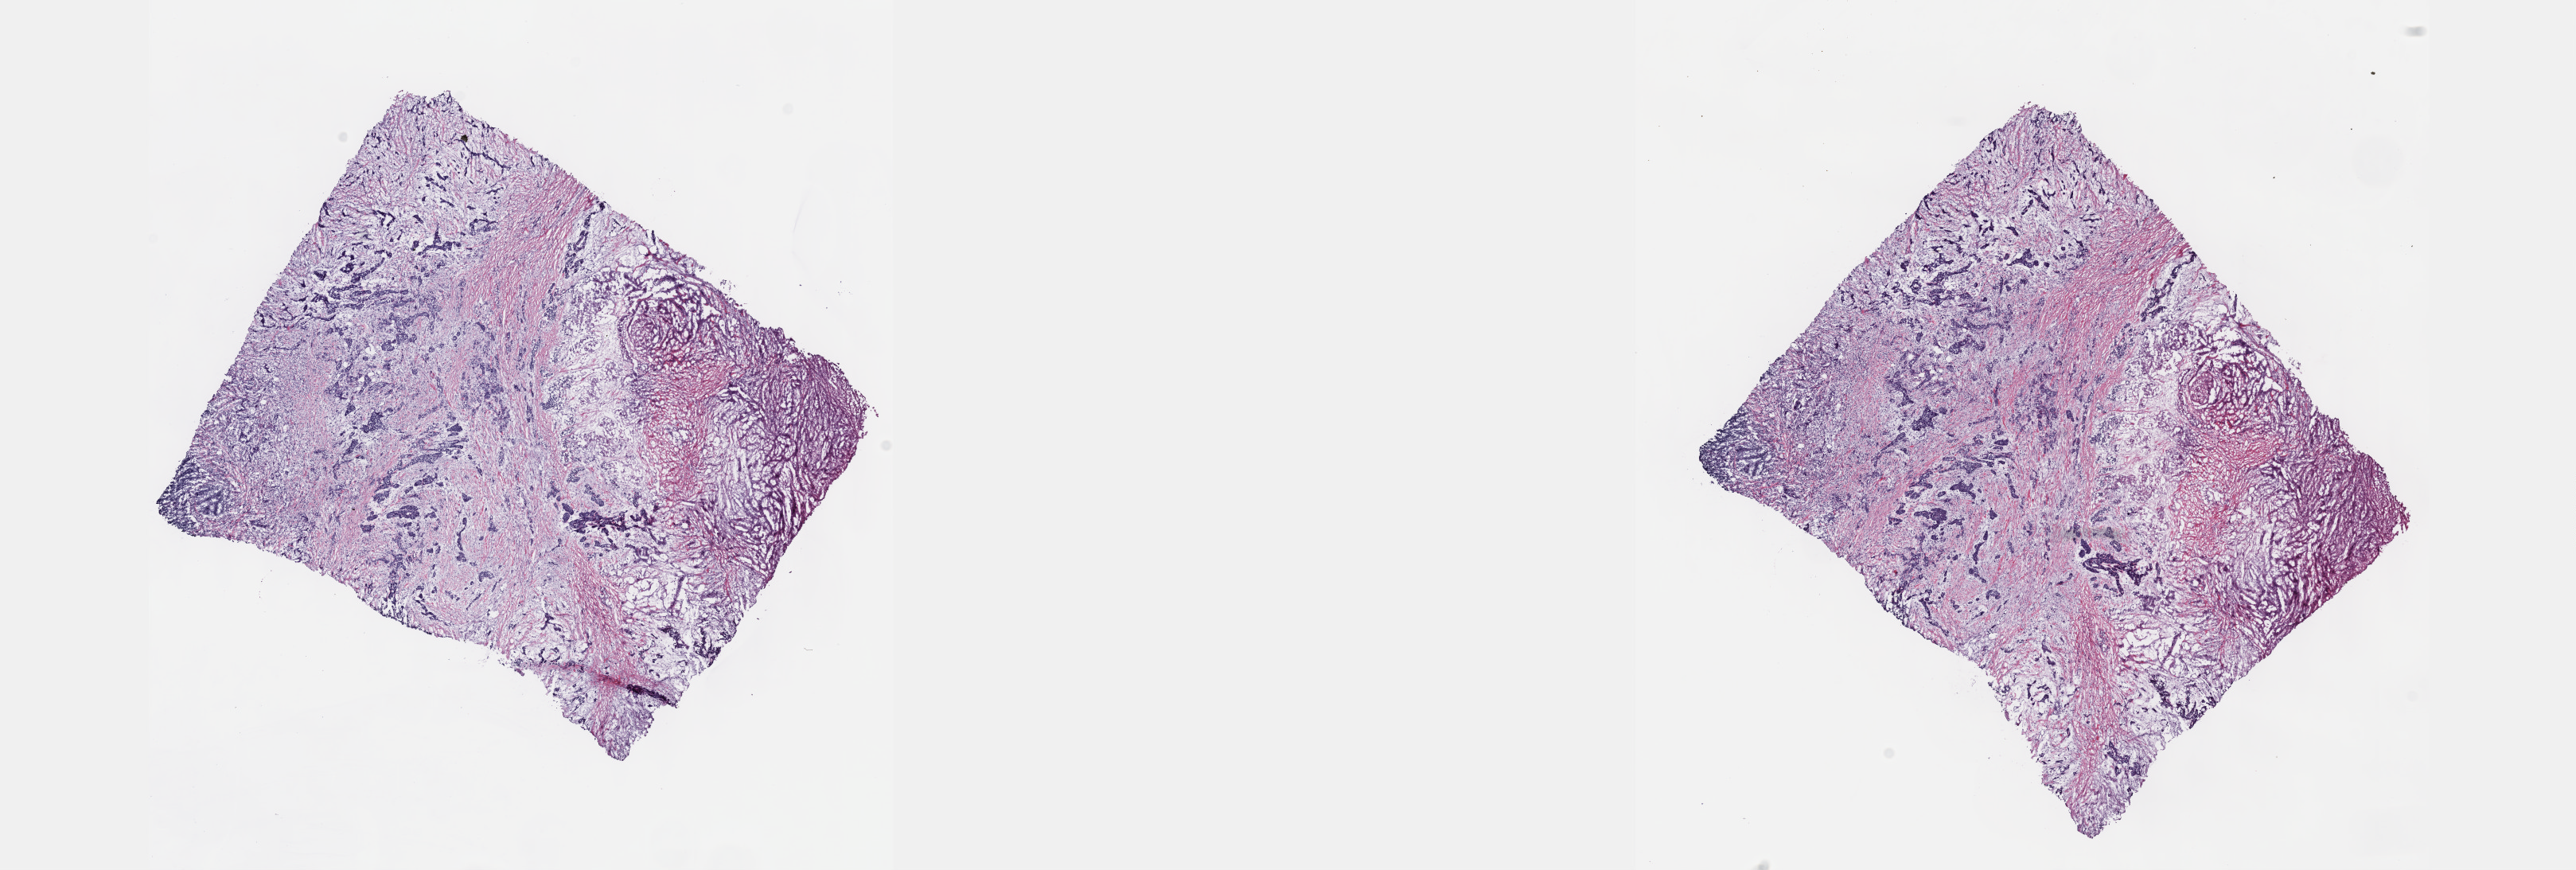
Hematoxylin and eosin (H&E) stained whole-slide image, whole scanned area (about 26.2 x 8.8 mm) shown as a low-resolution overview, frozen section from the top of the tissue portion, primary tumour sample from the pancreas. Female, age 55 years at initial diagnosis. Histologic grade: G3 (poorly differentiated). Slide review estimates, as recorded: tumour cells 30%, tumour nuclei 30%, normal cells 5%, stromal cells 40%, necrosis 25%. Infiltration values recorded for this section: lymphocyte infiltration 4%, monocyte infiltration 2%, neutrophil infiltration 9%.
TNM: T3 N0 M0. AJCC pathologic stage: IIA (7th edition). Lymph nodes positive (case pathology): 0 of 19 examined. Pathologic diagnosis: Adenocarcinoma, NOS (head of pancreas).